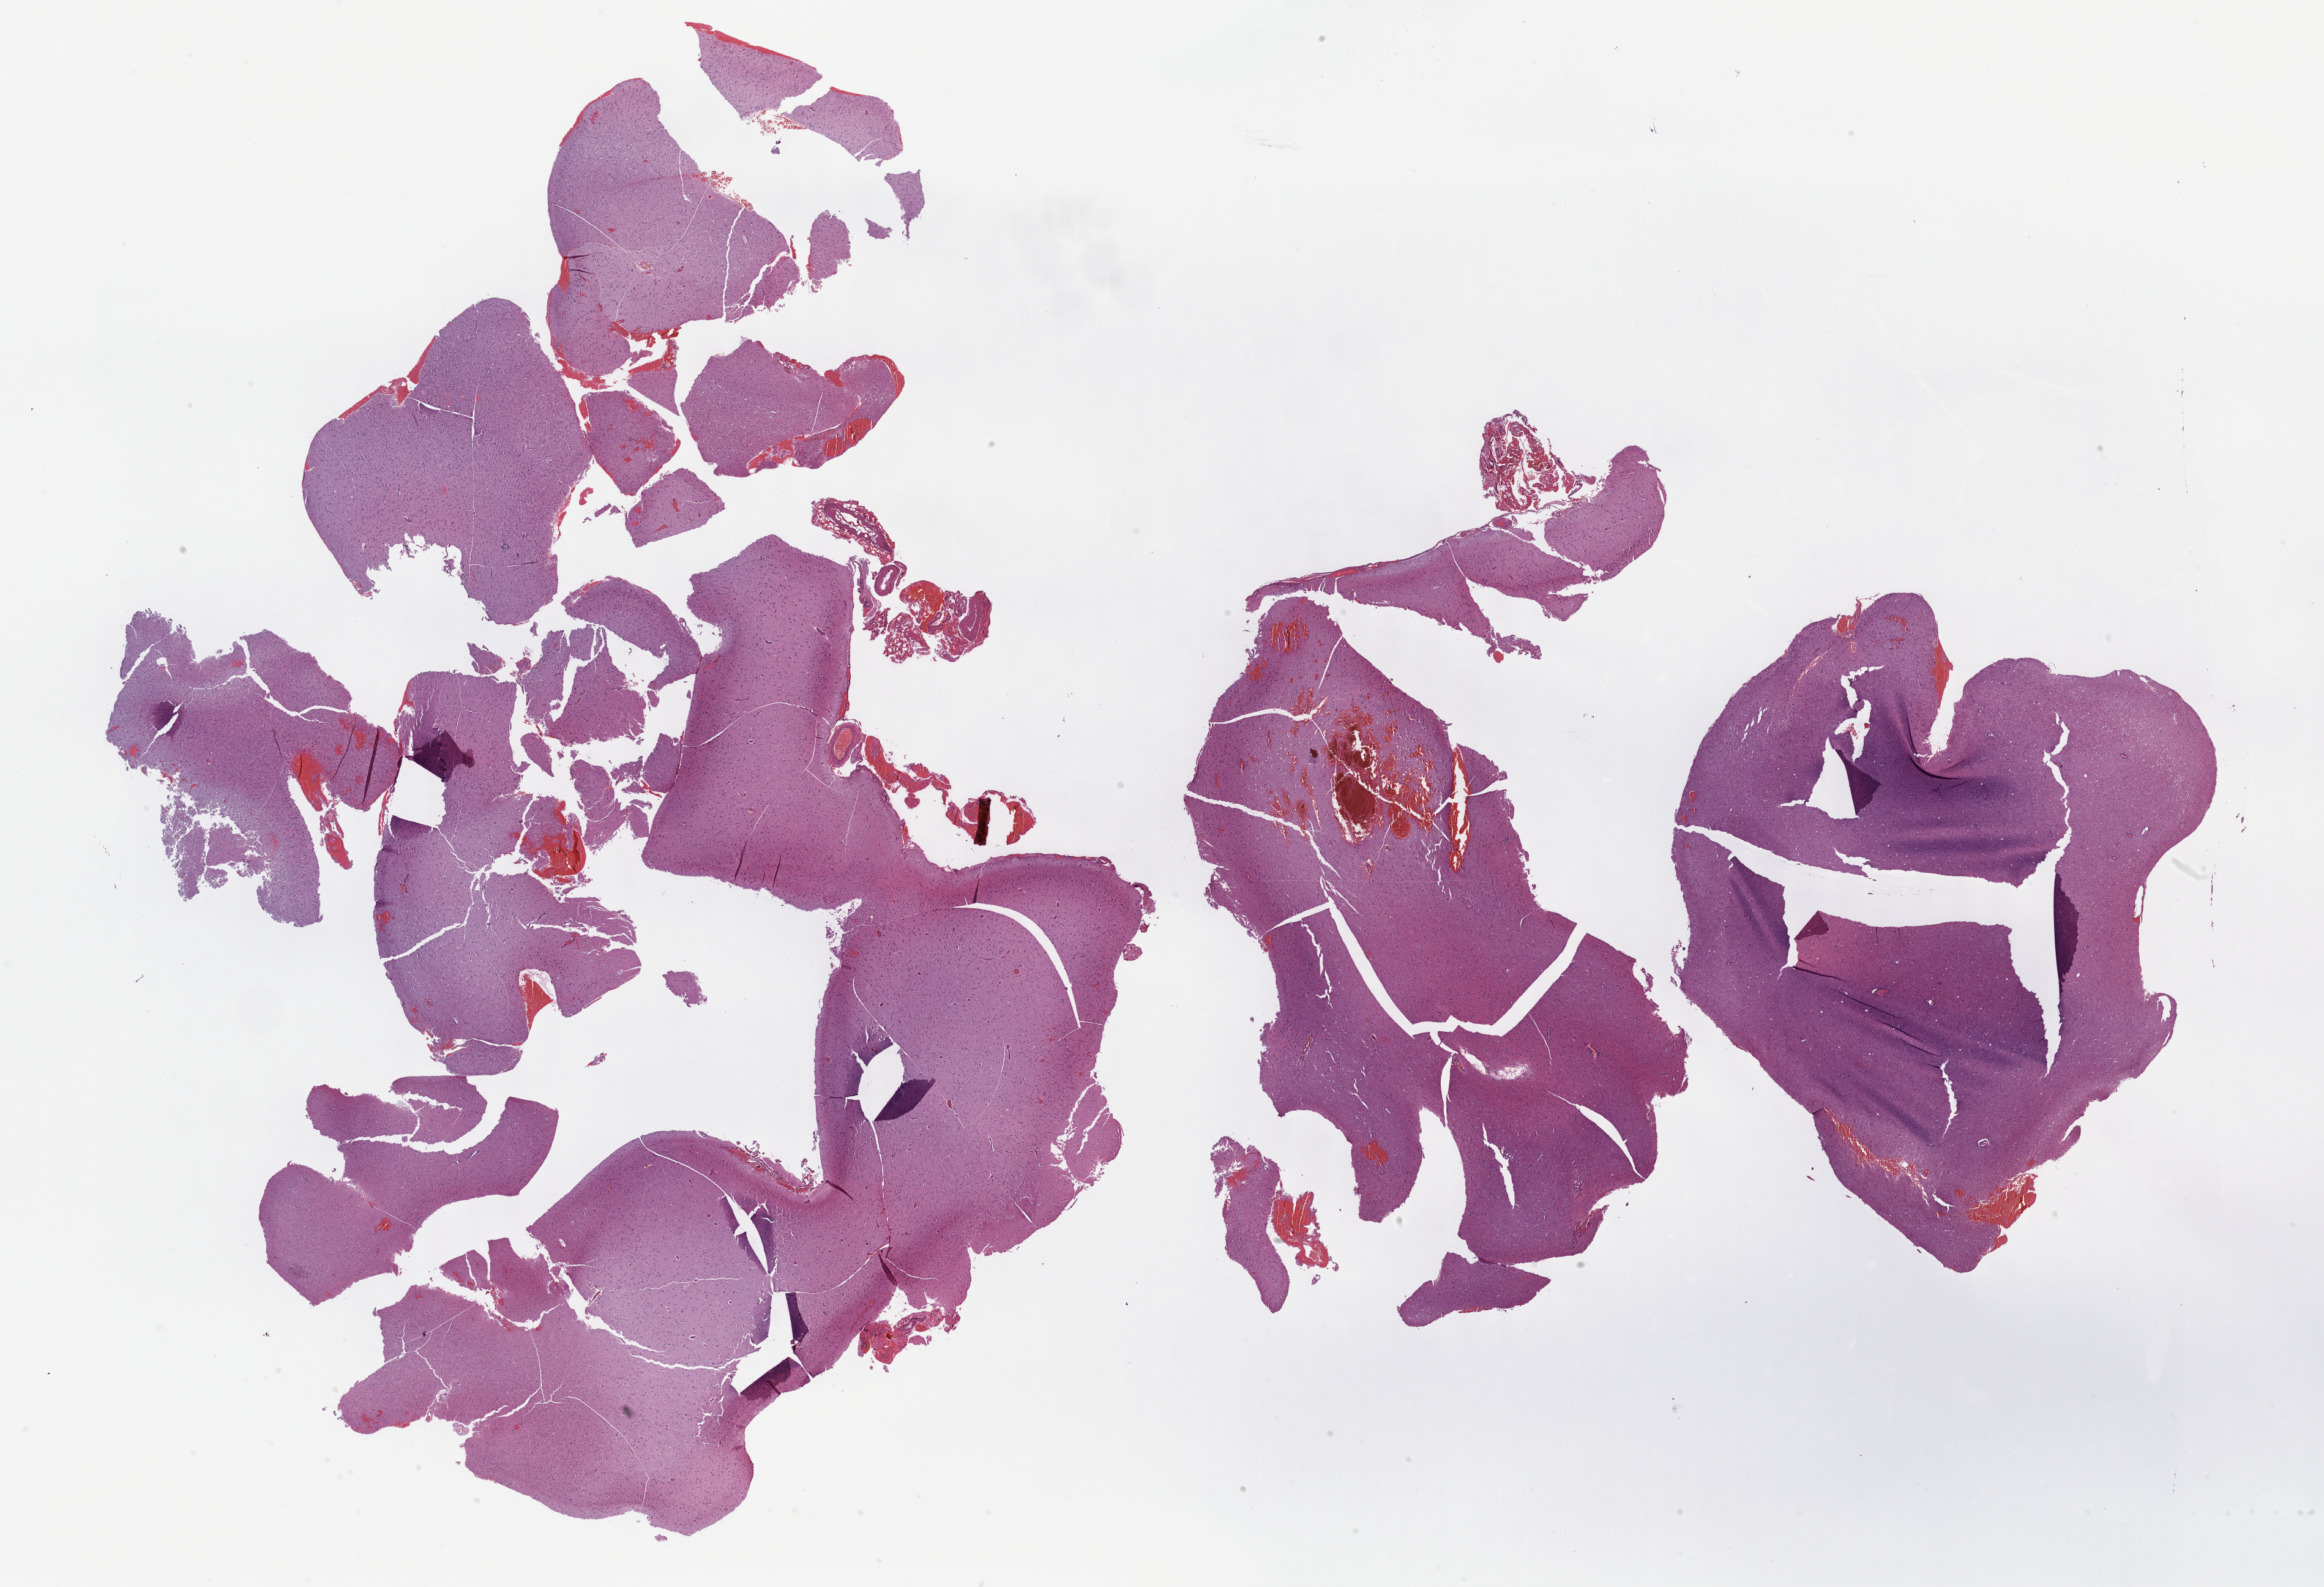
H&E-stained whole-slide image, shown as a low-resolution overview of the whole scanned area (about 30.7 x 21.0 mm), formalin-fixed paraffin-embedded (FFPE) diagnostic section, brain, primary tumour sample. Male, age 58 years at initial diagnosis. Histologic grade: G3 (poorly differentiated).
• pathologic diagnosis: Astrocytoma, anaplastic (cerebrum)
• laterality: right